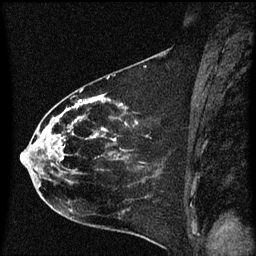
Breast MRI (dynamic contrast-enhanced), one sagittal slice; position 30 of 60 along the scan axis; dynamic contrast-enhanced series, image 2 of 3 at this slice position (ordered by acquisition); 1.5 T; TE 4.2 ms, TR 8.4 ms; 2 mm slice thickness; 256 × 256 image matrix. Patient: female, 35 years. Case-level facts recorded for this patient, not image findings: setting: breast cancer imaged before/during neoadjuvant chemotherapy; receptor status: HER2-positive.
Outlined on this slice (semi-automatic segmentation, software-assisted and operator-edited):
- analysis volume of interest (the breast-tissue region the enhancement analysis was run in; not a lesion): bounding box [x1, y1, x2, y2] px = [21, 68, 173, 173]
- tumour enhancement mask (voxels above the 70 % enhancement threshold inside the analysis volume of interest): [34, 96, 106, 173]